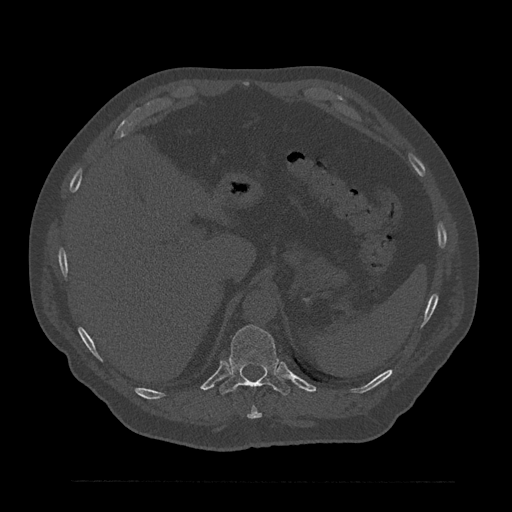
CT including the spine, one axial slice; position 305 of 797 along the scan axis; reconstruction kernel Br40s/3; bone window (W 1800 / L 400 HU); 0.5 mm slice thickness; 512 × 512 image matrix, field of view 430 × 430 mm. Male patient, age 61 years. From the clinical record (not read from this slice): primary cancer: prostate.
Structures marked on this image (semi-automatically segmented with operator editing):
- T10 vertebra: bounding box <247,405,262,419> (left, top, right, bottom; pixels)
- T11 vertebra: <220,325,290,396>